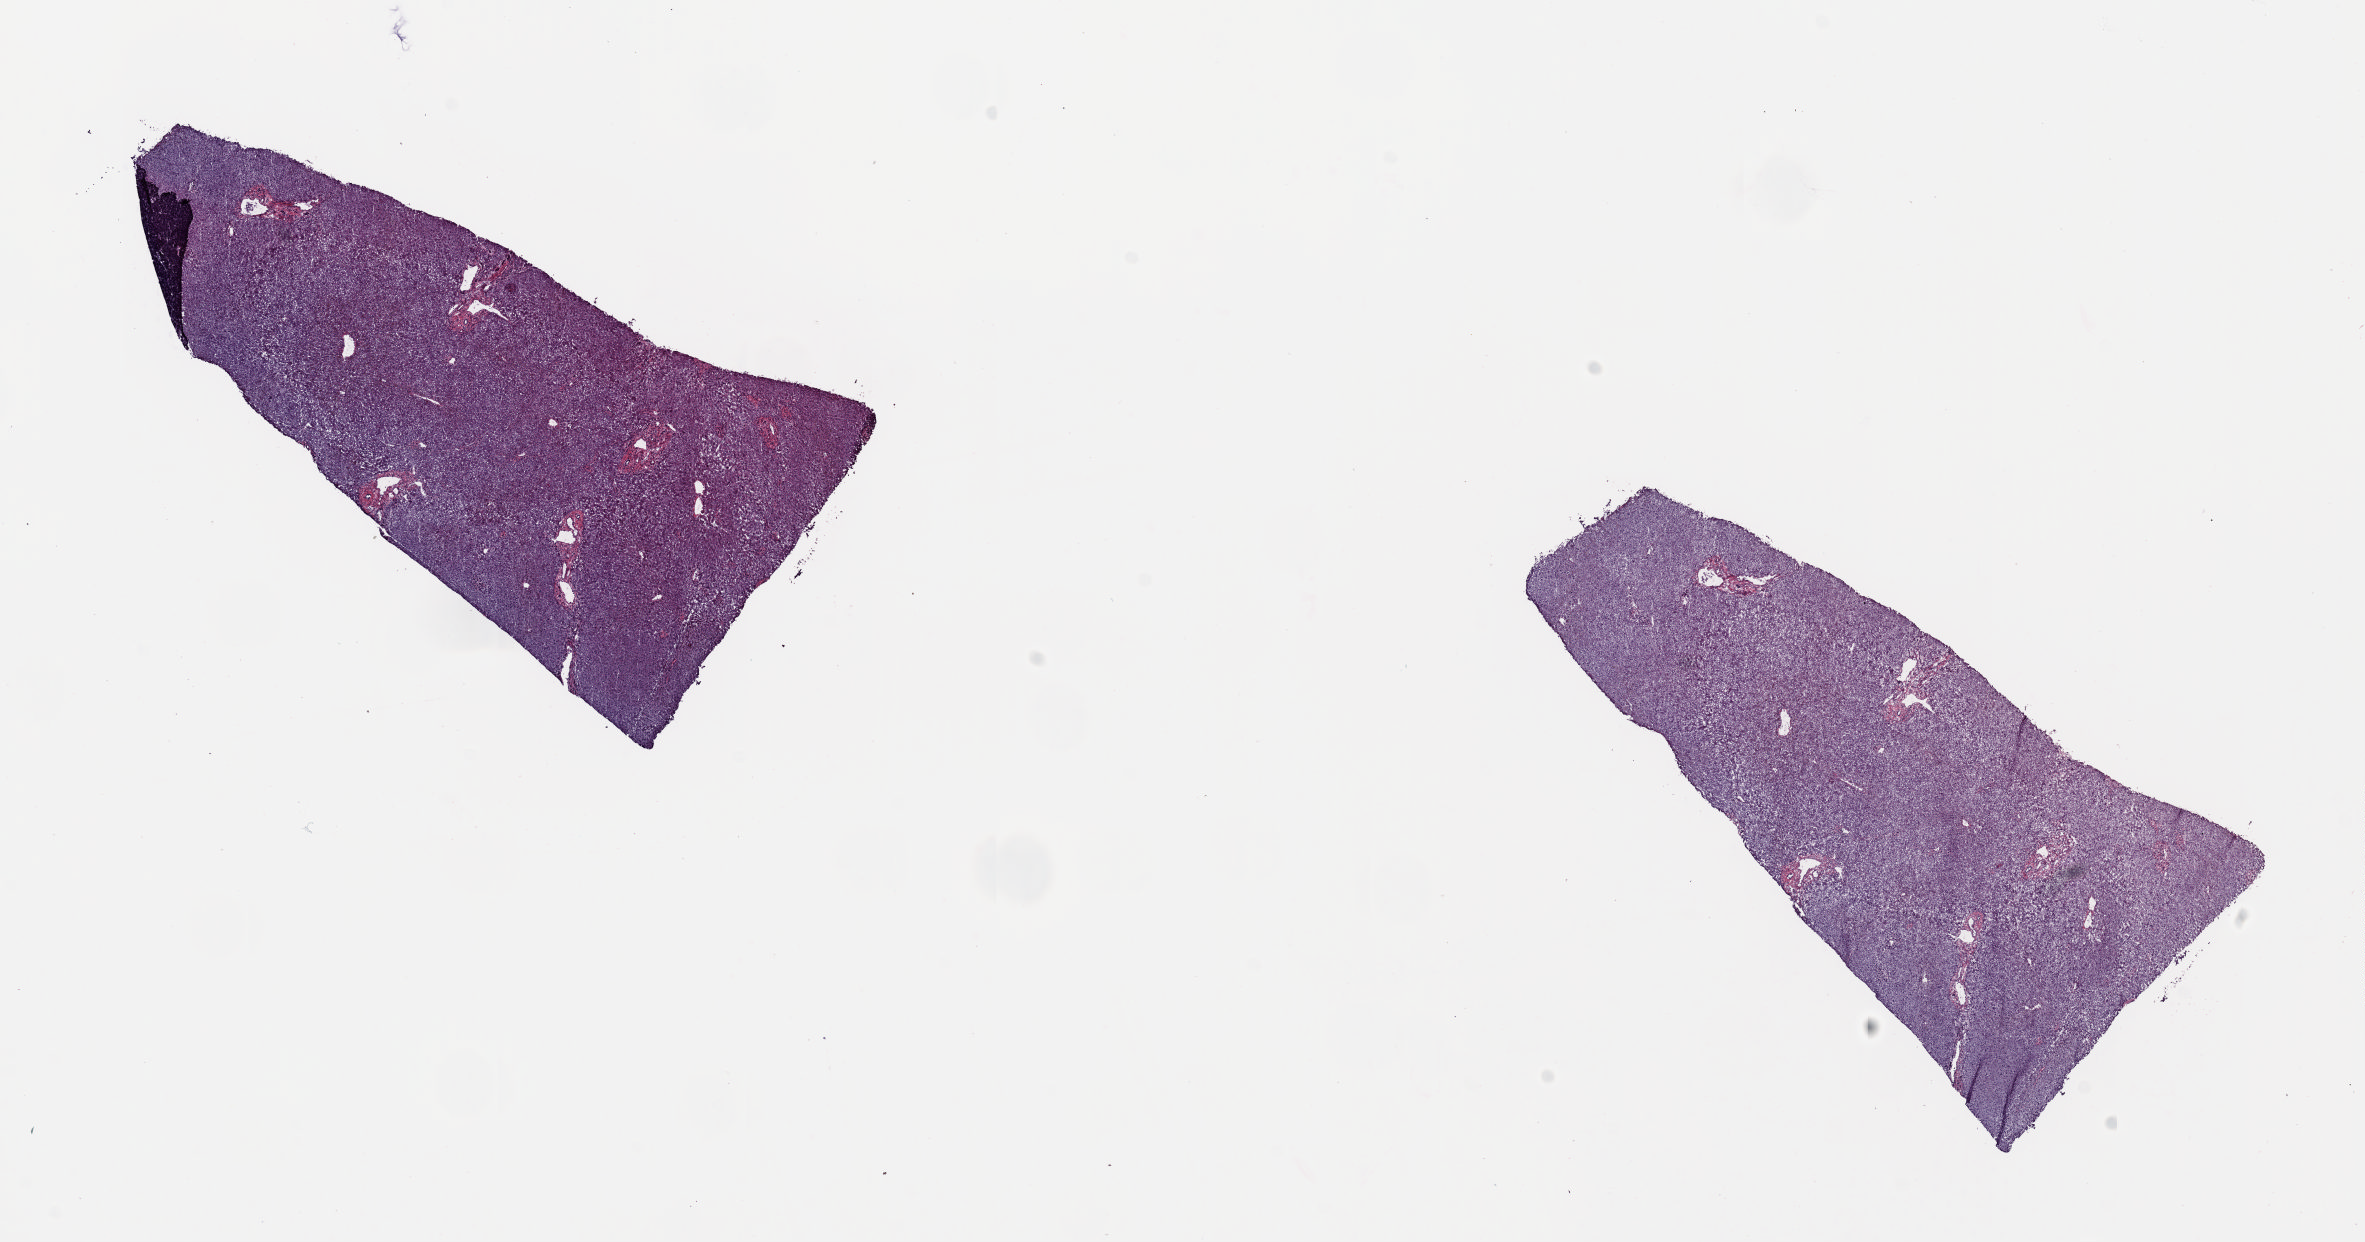
H&E whole-slide image, low-resolution overview of the scanned area, about 18.6 x 9.8 mm; frozen section from the top of the tissue portion; solid tissue normal (non-tumour tissue) sample from the liver. Patient: female, age at initial diagnosis 56 years. Pathologist review of this section (percent, as recorded): tumour cells 0%, tumour nuclei 0%, normal cells 100%, stromal cells 0%, necrosis 0%. Infiltration values recorded for this section: lymphocyte infiltration 2%, monocyte infiltration 0%, neutrophil infiltration 0%.
This section: solid tissue normal sample (biorepository sample class). Patient diagnosis: Hepatocellular carcinoma, NOS.